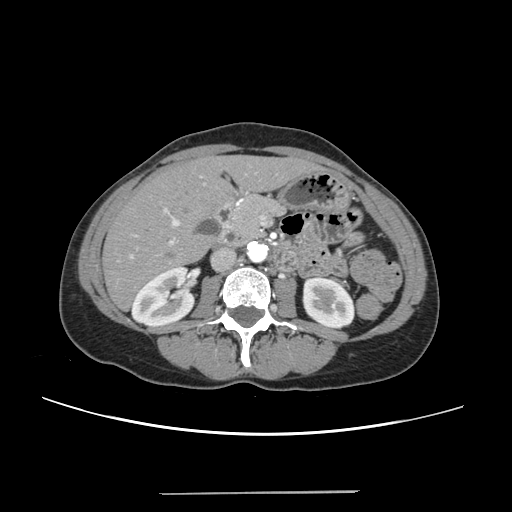
Contrast-enhanced abdominal CT, one axial slice; position 103 of 240 along the scan axis; 120 kVp; intravenous contrast given; soft-tissue window (W 400 / L 40 HU); 1.25 mm slice thickness; 512 × 512 image matrix. Female patient, age 60 years. From the clinical record (not read from this slice): diagnosis: colorectal cancer liver metastases, imaged before liver resection; multiple liver metastases: no; largest metastasis: 1.5 cm; disease in both lobes: no.
Annotated regions visible in this slice (expert manual segmentation):
- liver: bounding box [x1, y1, x2, y2] px = [105, 157, 313, 308]
- planned liver remnant (the part of the liver to remain after resection): [105, 158, 315, 308]
- portal vein (with intrahepatic branches): [118, 175, 242, 261]